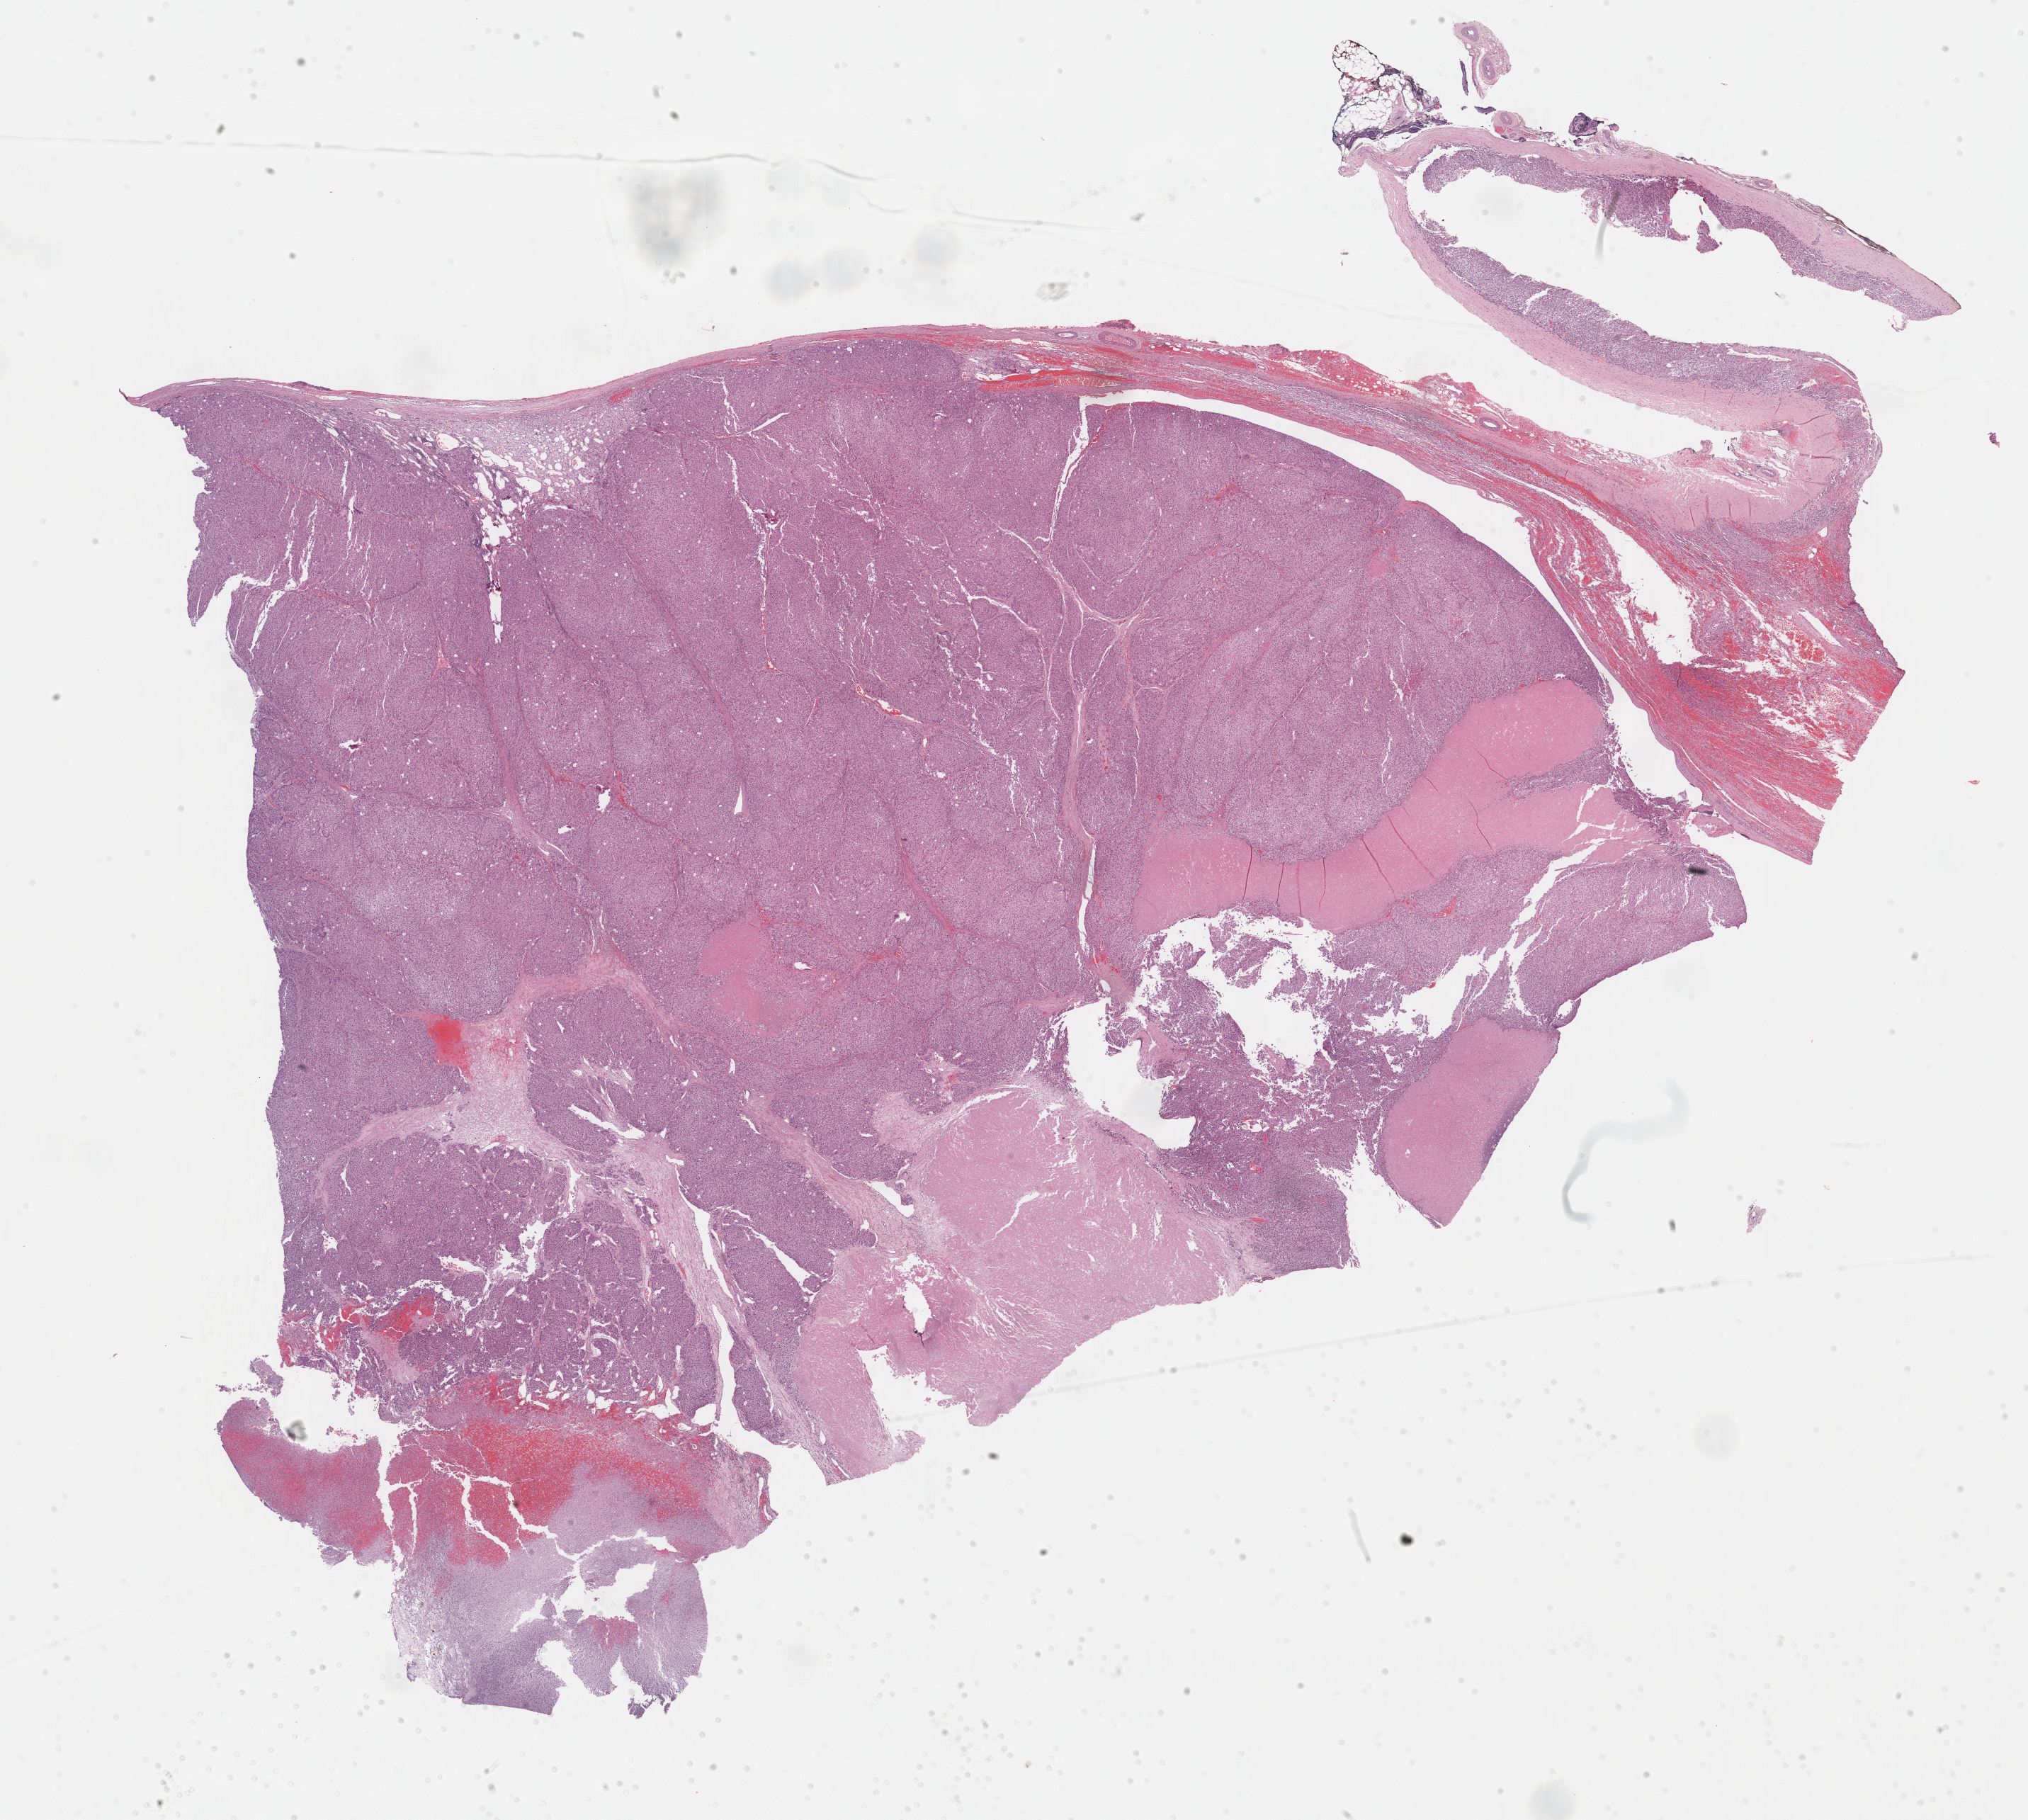
Hematoxylin and eosin (H&E) stained whole-slide image — whole scanned area (about 23.2 x 20.8 mm, from a 40x scan) shown as a low-resolution overview, formalin-fixed paraffin-embedded (FFPE) diagnostic section, sample: primary tumour, adrenal cortex. Female, age 65 years at initial diagnosis.
Histologic diagnosis: Adrenal cortical carcinoma (cortex of adrenal gland).